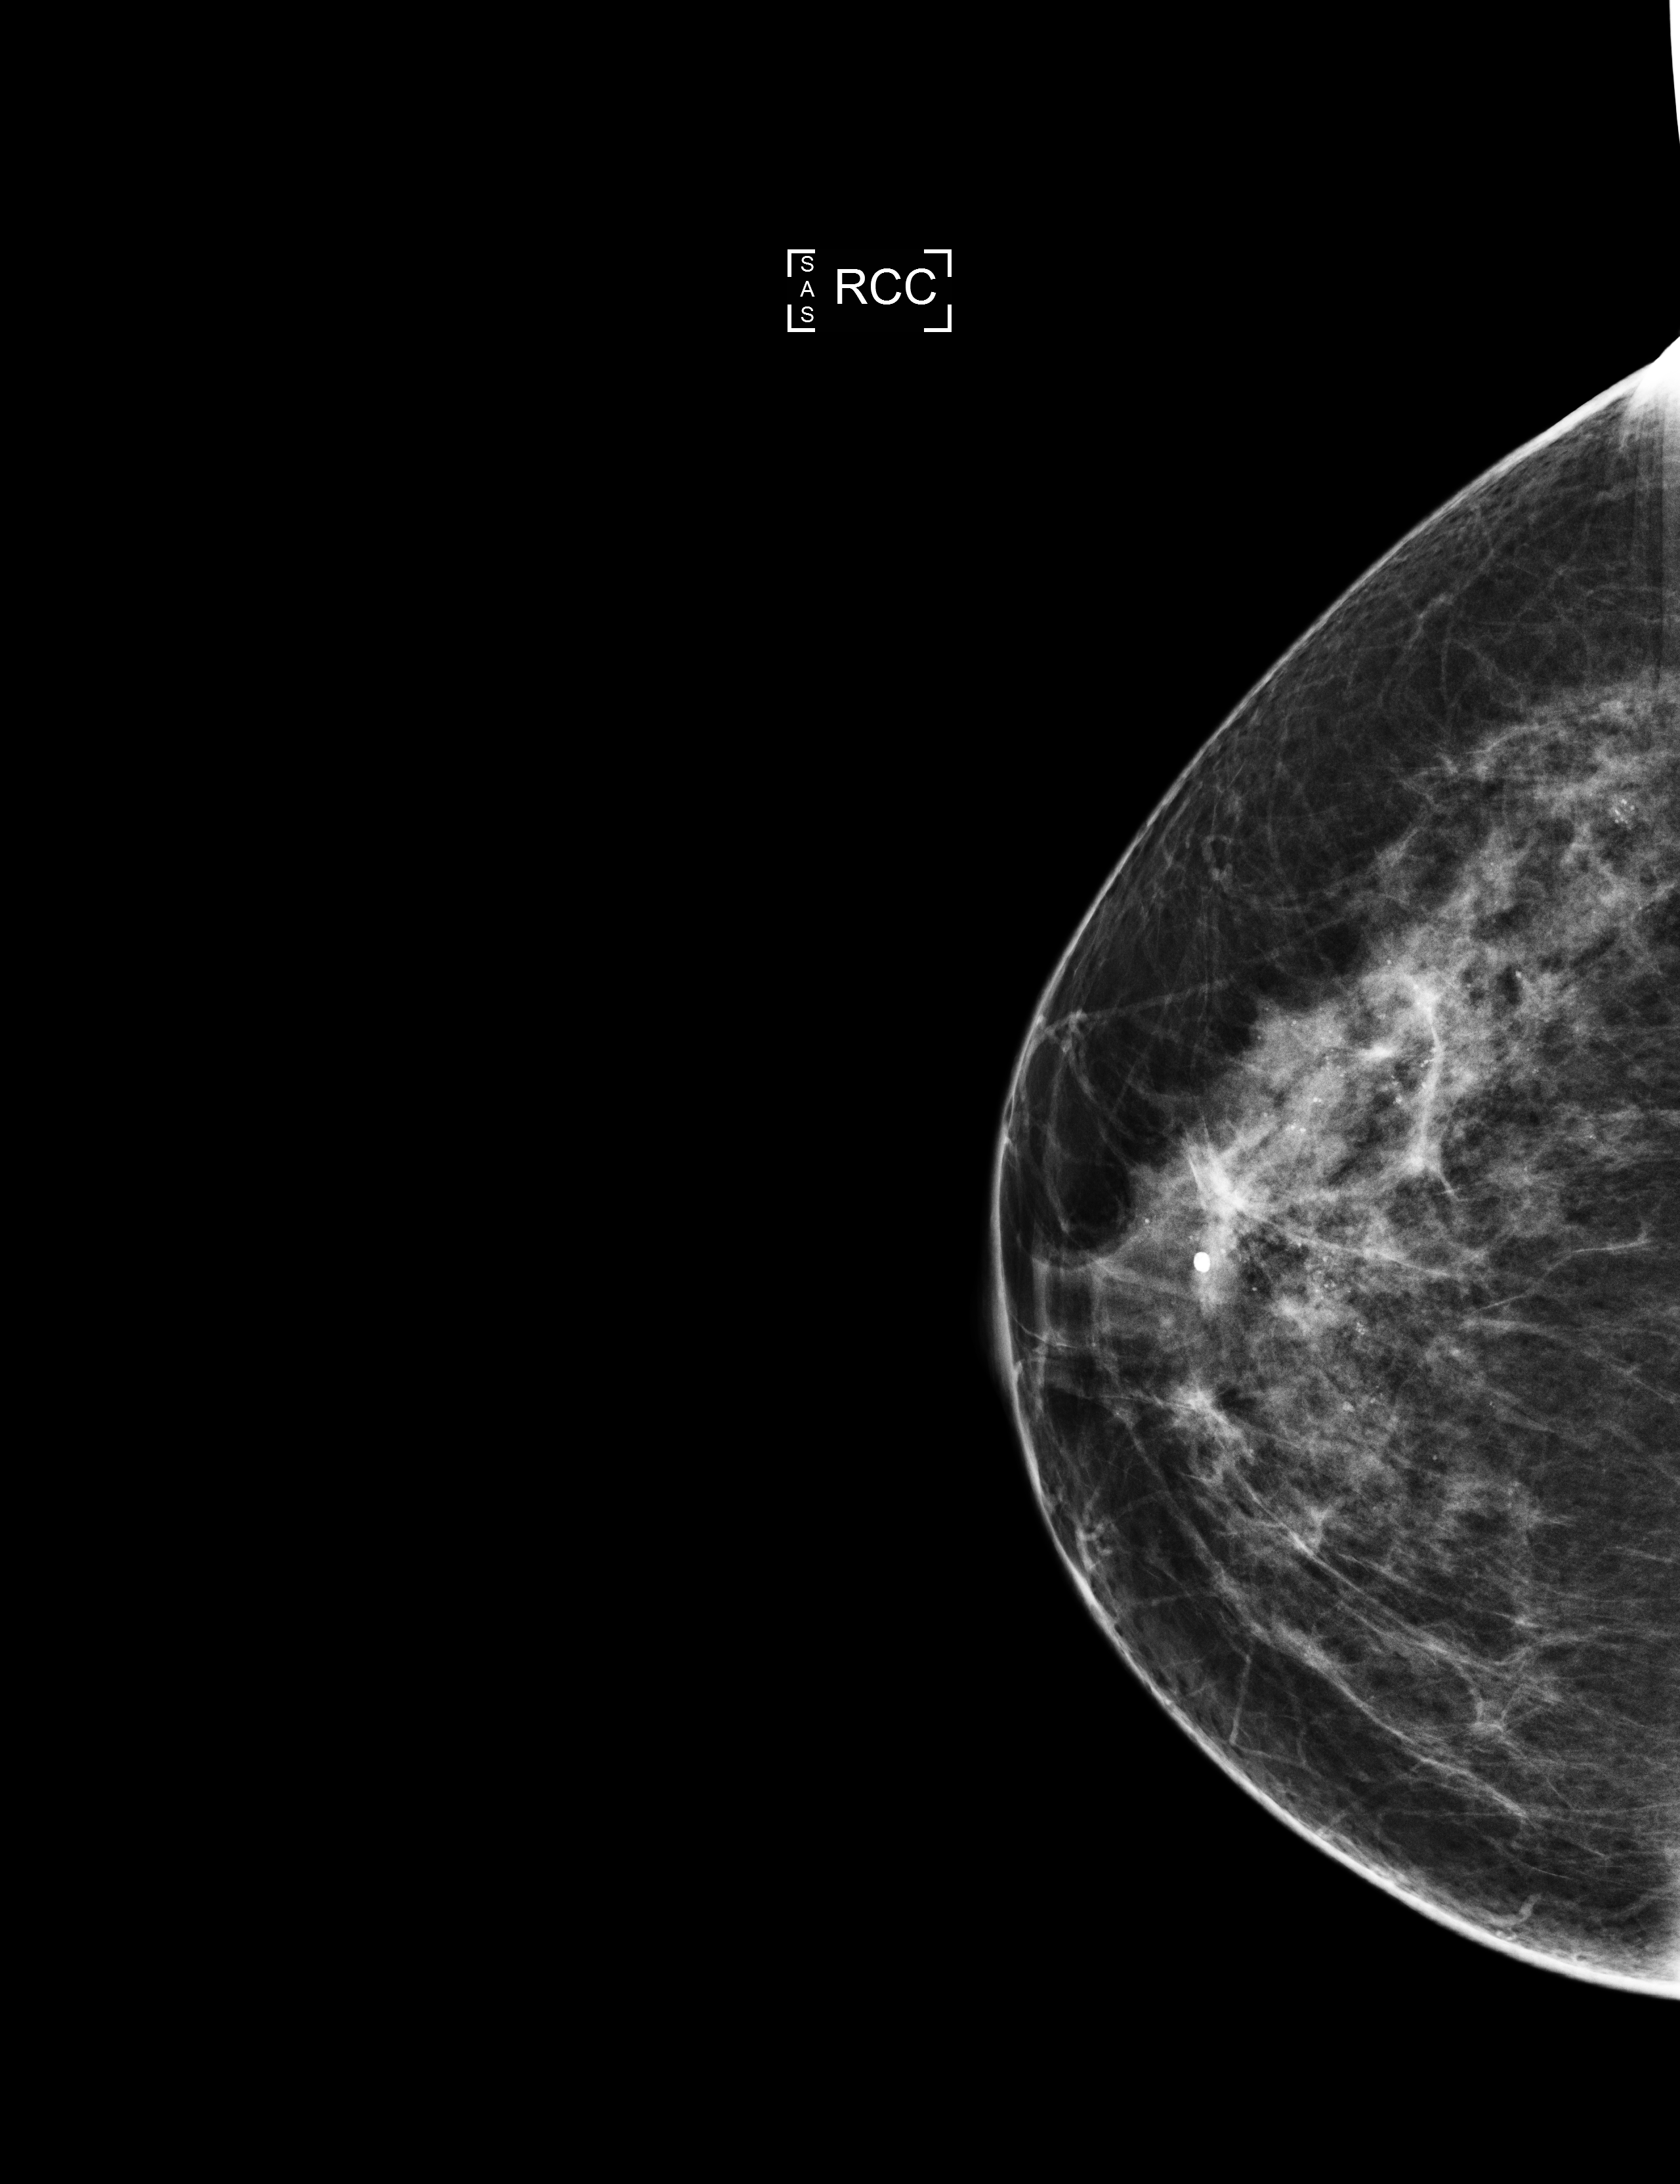
Screening examination; compressed breast thickness 59 mm; system: Selenia Dimensions. Female patient, age 51 years.
Image type: full-field digital mammogram. Breast: right. Projection: craniocaudal (CC) view.